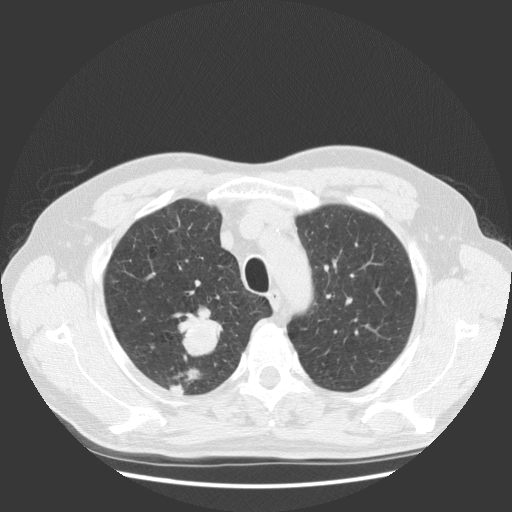
Low-dose screening chest CT, axial slice. Baseline annual screen. Lung window (W 1500 / L -600 HU). 2.5 mm slice thickness. Standard (soft-tissue) reconstruction kernel (STANDARD). Slice 101 of 131 in the series. 512 × 512 image matrix. Male participant, aged 63 years at enrolment. Current smoker at enrolment.
Lesion marked by an expert reader, bounding box [x1, y1, x2, y2] px = [160, 308, 232, 379]. The screening reader recorded 2 non-calcified nodules or masses ≥4 mm on this exam (right upper lobe, right upper lobe); which of them this box marks is not recorded.